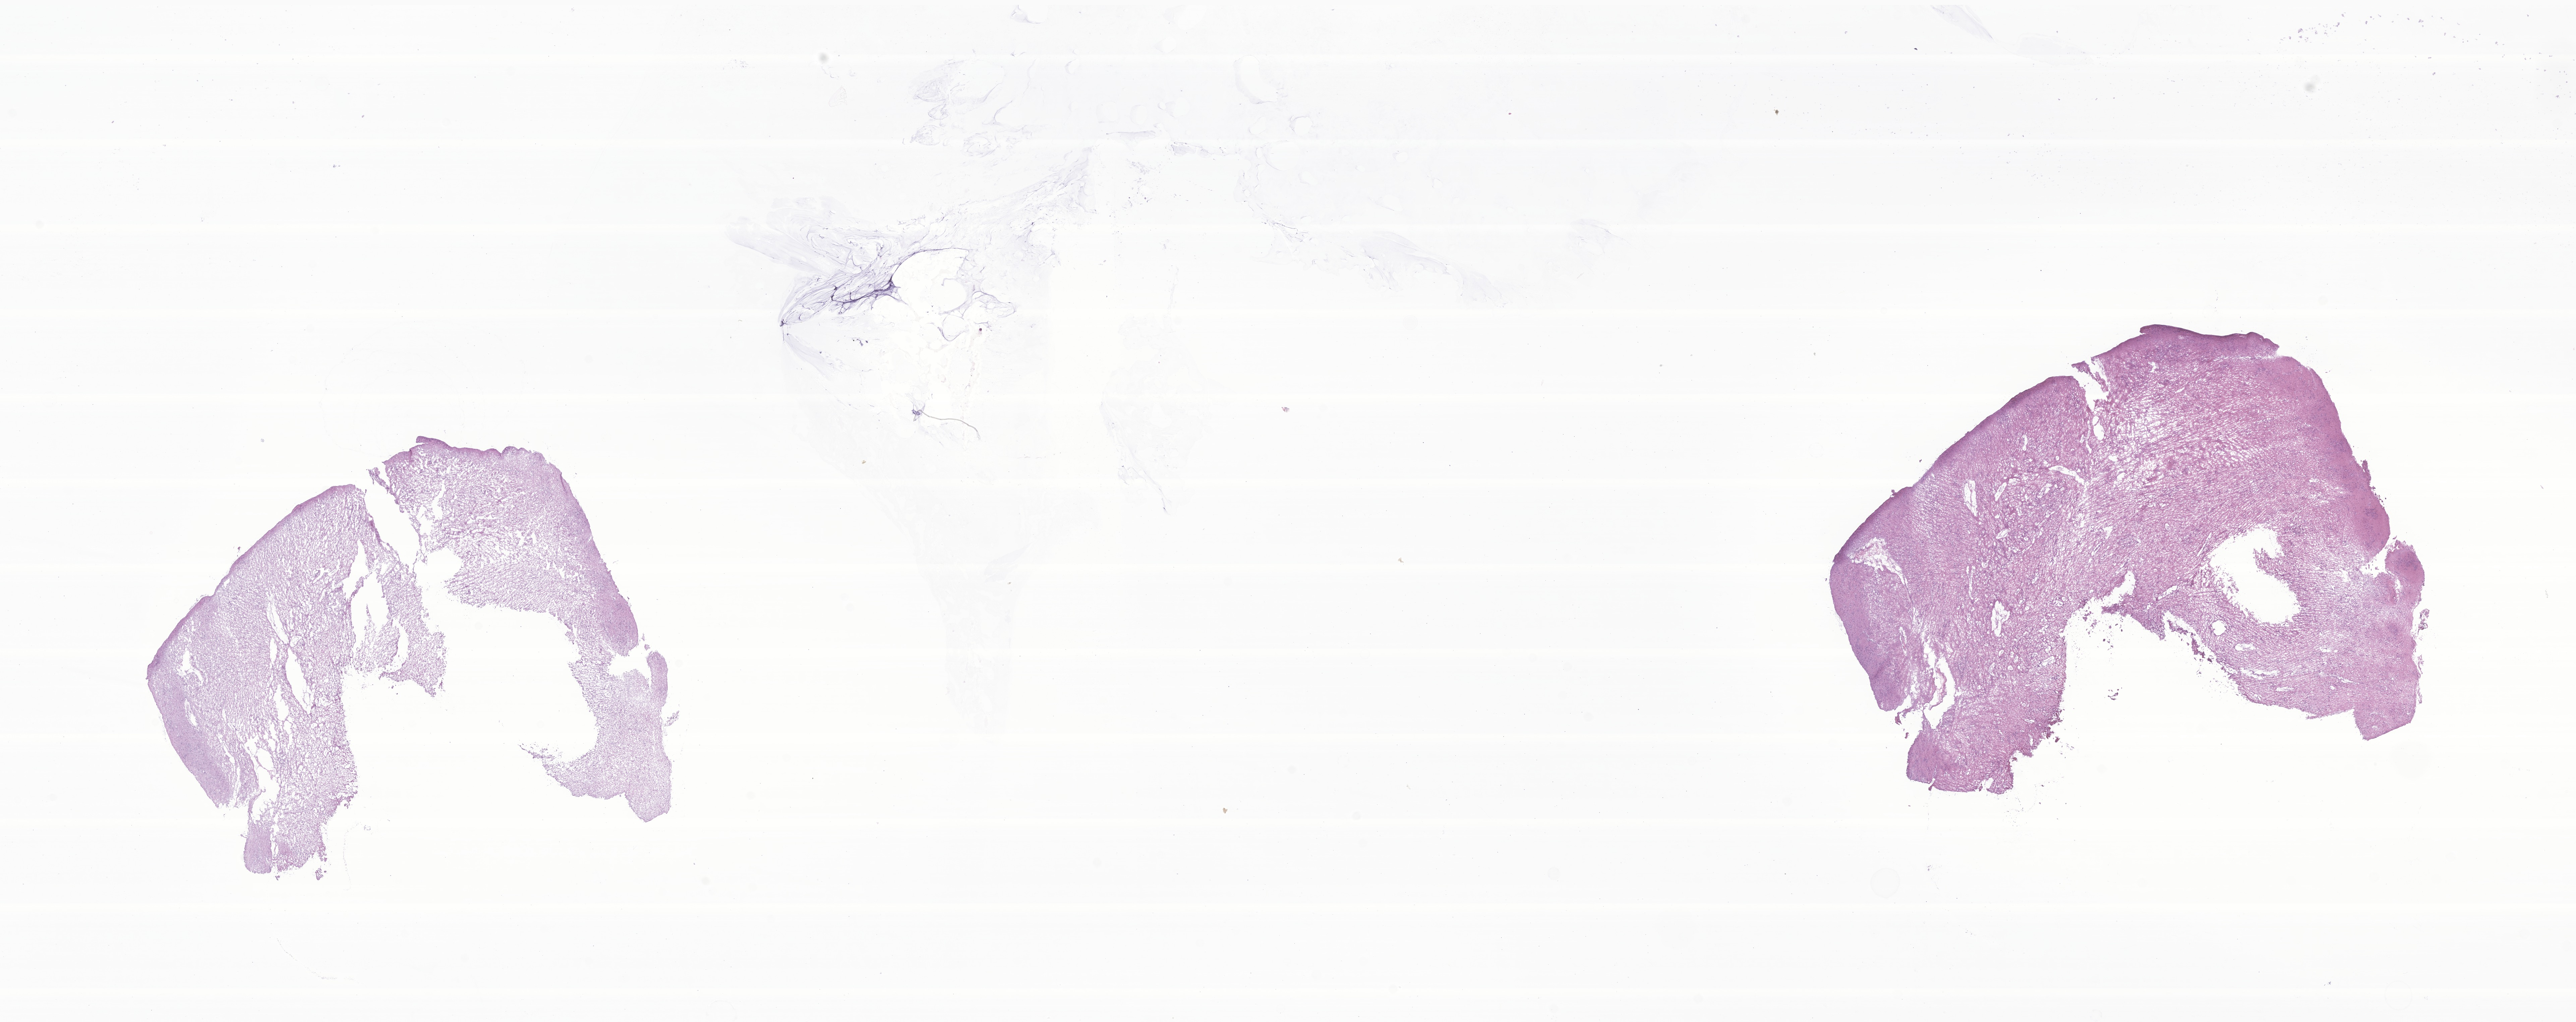
Whole-slide image, hematoxylin and eosin (H&E) stain of tumor tissue from the brain, shown as a low-resolution overview of the whole scanned area (about 32.4 x 12.9 mm); frozen section. Patient male; age 245 months.
• recorded diagnosis: Subependymoma